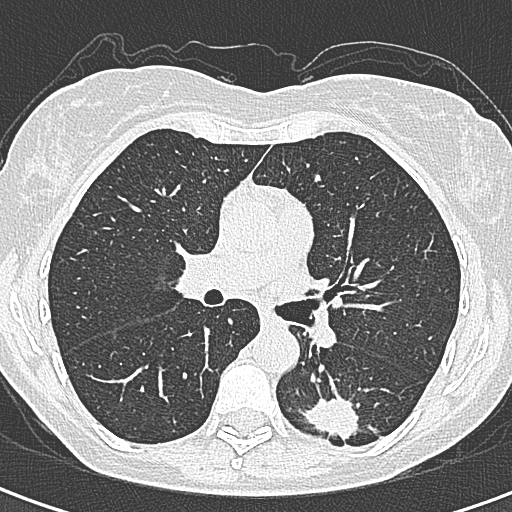
Low-dose screening chest CT, axial slice. First (baseline) screen. Lung window (W 1500 / L -600 HU). 512 × 512 image matrix. Female, age 58 years at enrolment.
• Expert reader's lesion annotation, box from (x=296, y=387) to (x=366, y=455) px.
• The screening reader recorded 2 non-calcified nodules or masses ≥4 mm on this exam; which of them this box marks is not recorded.
• Official screen result: positive, change unspecified: nodule(s) >= 4 mm or enlarging nodule(s), mass(es), or other non-specific abnormalities suspicious for lung cancer.
• Participant outcome: lung cancer diagnosed 22 days after this screen — adenocarcinoma, NOS, left lower lobe, moderately differentiated (G2), stage IA (AJCC 6th edition), 25 mm at pathology.